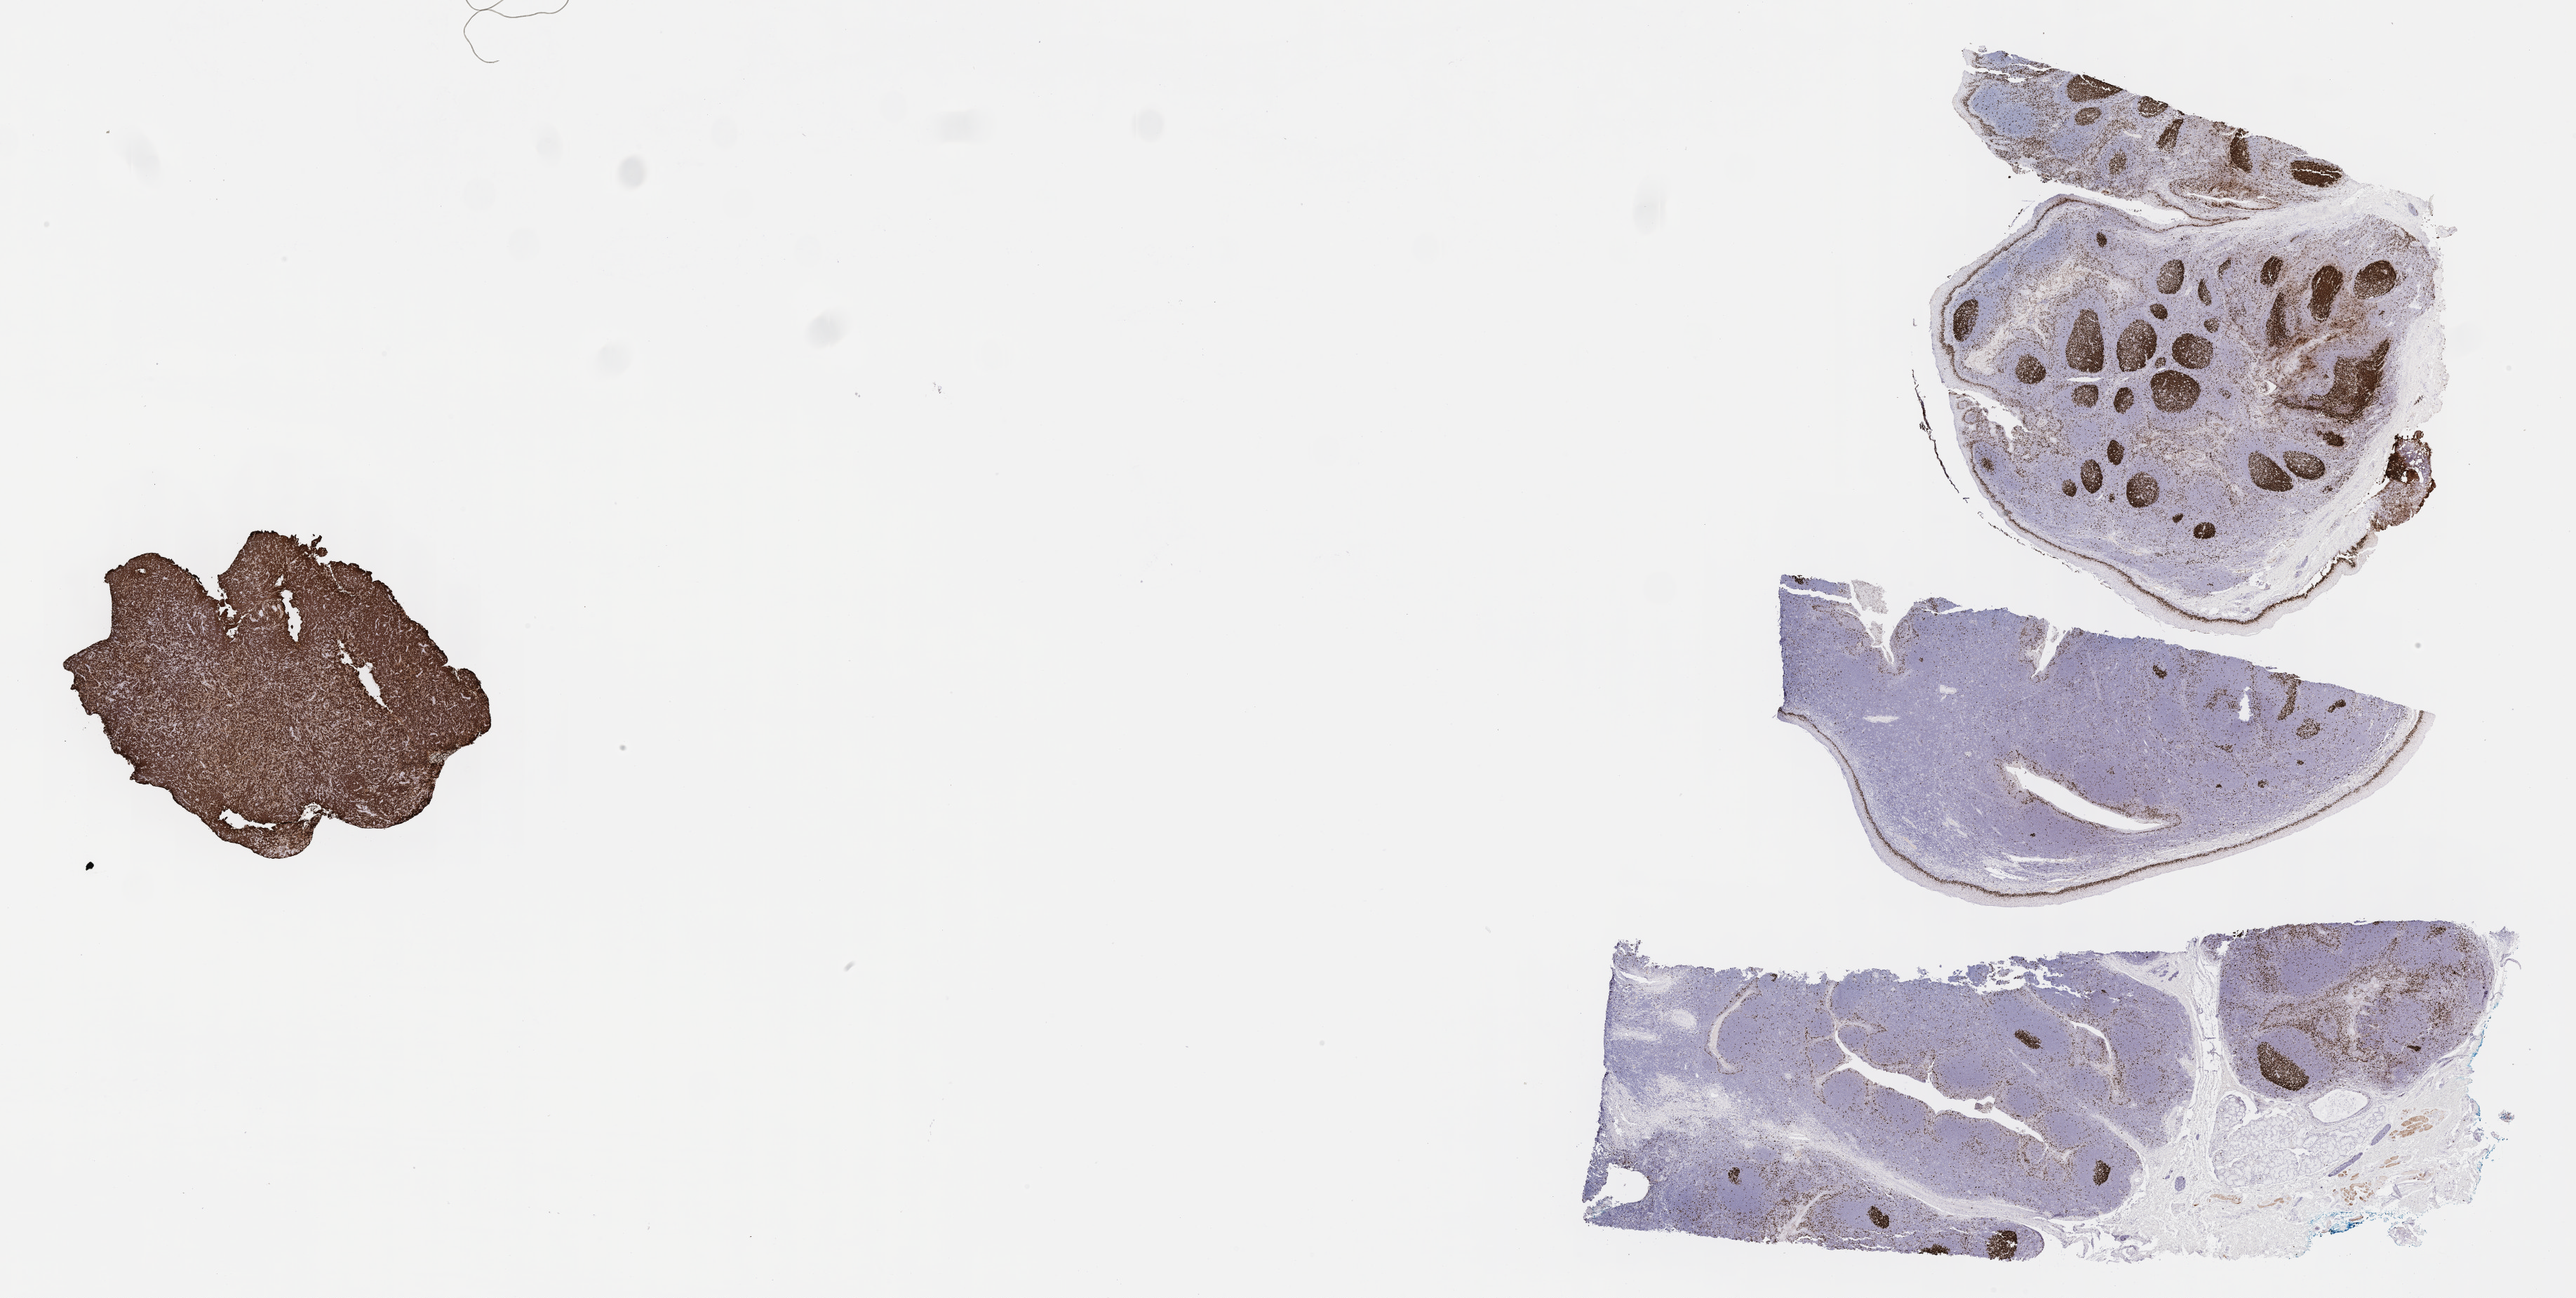
Whole-slide image, immunohistochemical stain for Ki-67, a low-resolution overview of the entire scanned area, about 29.7 x 15.0 mm, tumor tissue, site: mandible. Male patient; age at initial diagnosis 8 years.
Diagnosis: Burkitt lymphoma, NOS.